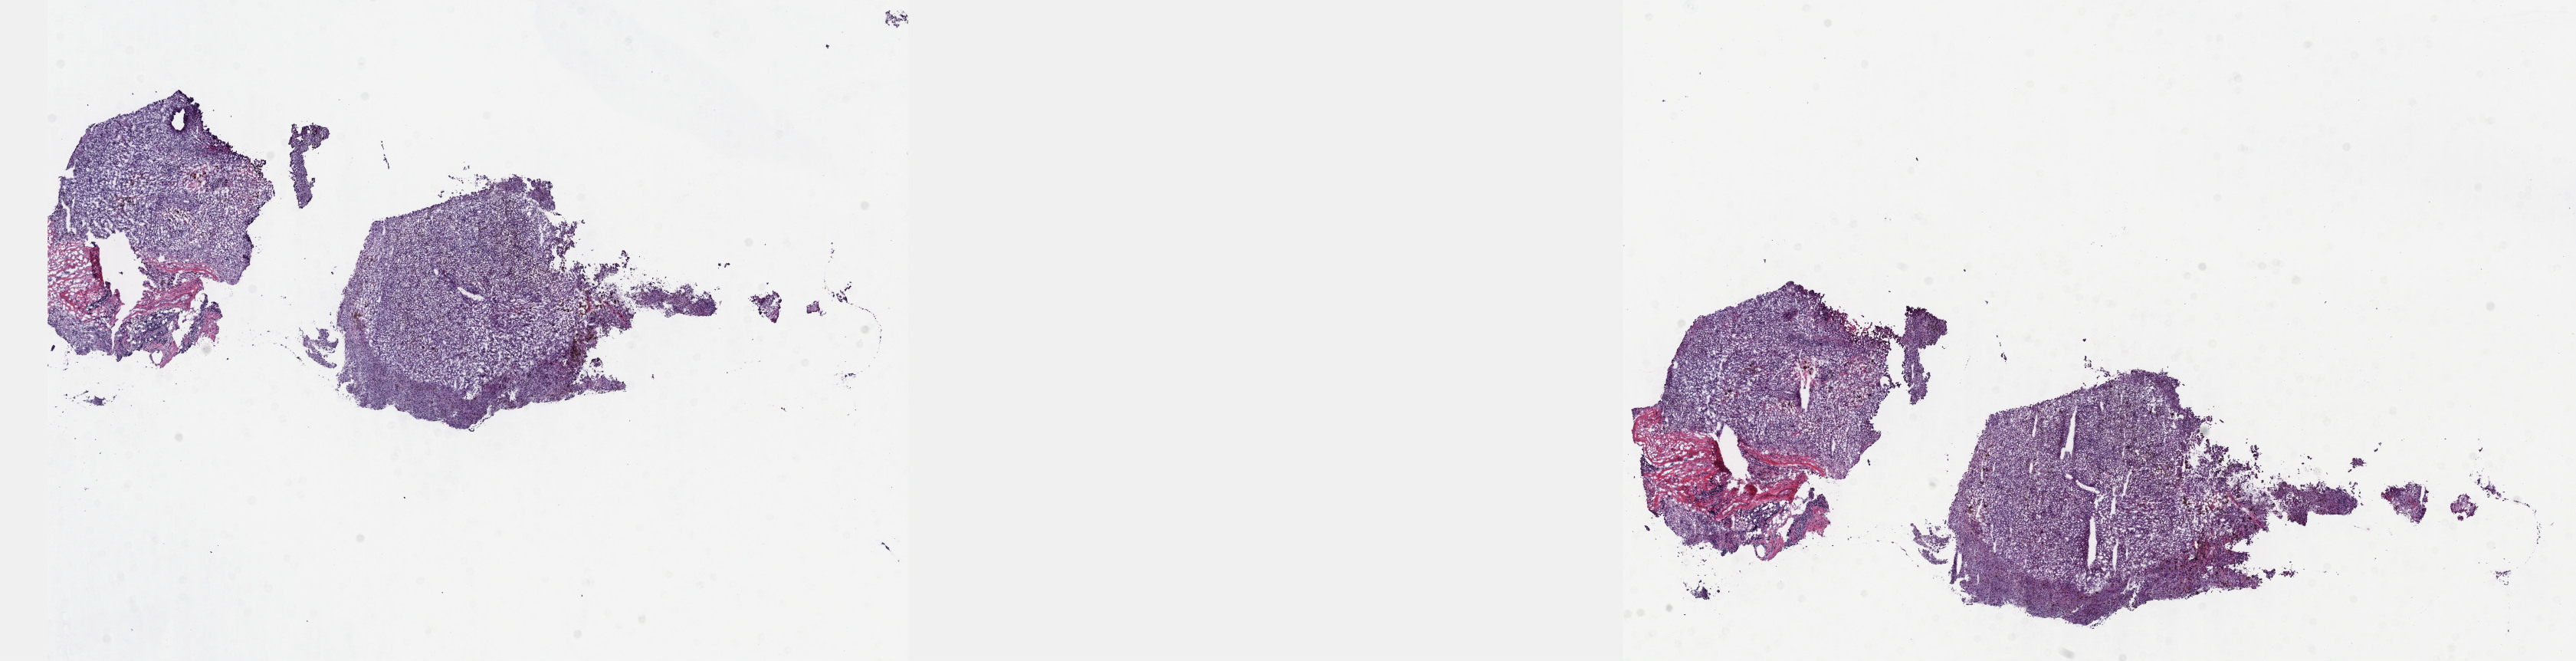
Hematoxylin and eosin (H&E) stained whole-slide image — a low-resolution overview of the entire scanned area, about 27.2 x 7.0 mm (acquisition: 40x scan); frozen section from the top of the tissue portion; metastatic tumour sample, sampled site: lymph nodes of head, face and neck. Female, age 83 years at initial diagnosis.
This section: metastatic tumour tissue. Patient diagnosis: Malignant melanoma, NOS.